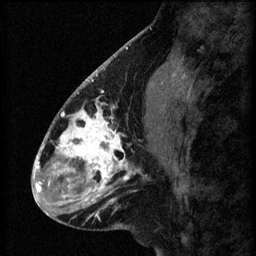
Breast MRI (dynamic contrast-enhanced), one sagittal slice. Slice 25 of 60 in the series (ordered by position). 3 images stored at this slice position (order not interpretable as contrast timing). 1.5 T. TE 4.2 ms, TR 8.2 ms. 2.2 mm slice thickness. 256 × 256 image matrix, field of view 180 × 180 mm. Female patient, age 41 years.
Structures marked on this image (semi-automatic segmentation, software-assisted and operator-edited):
- analysis volume of interest (the breast-tissue region the enhancement analysis was run in; not a lesion): box from (x=56, y=104) to (x=157, y=207) px
- tumour enhancement mask (voxels above the 70 % enhancement threshold inside the analysis volume of interest): (x=56, y=104)–(x=136, y=207)